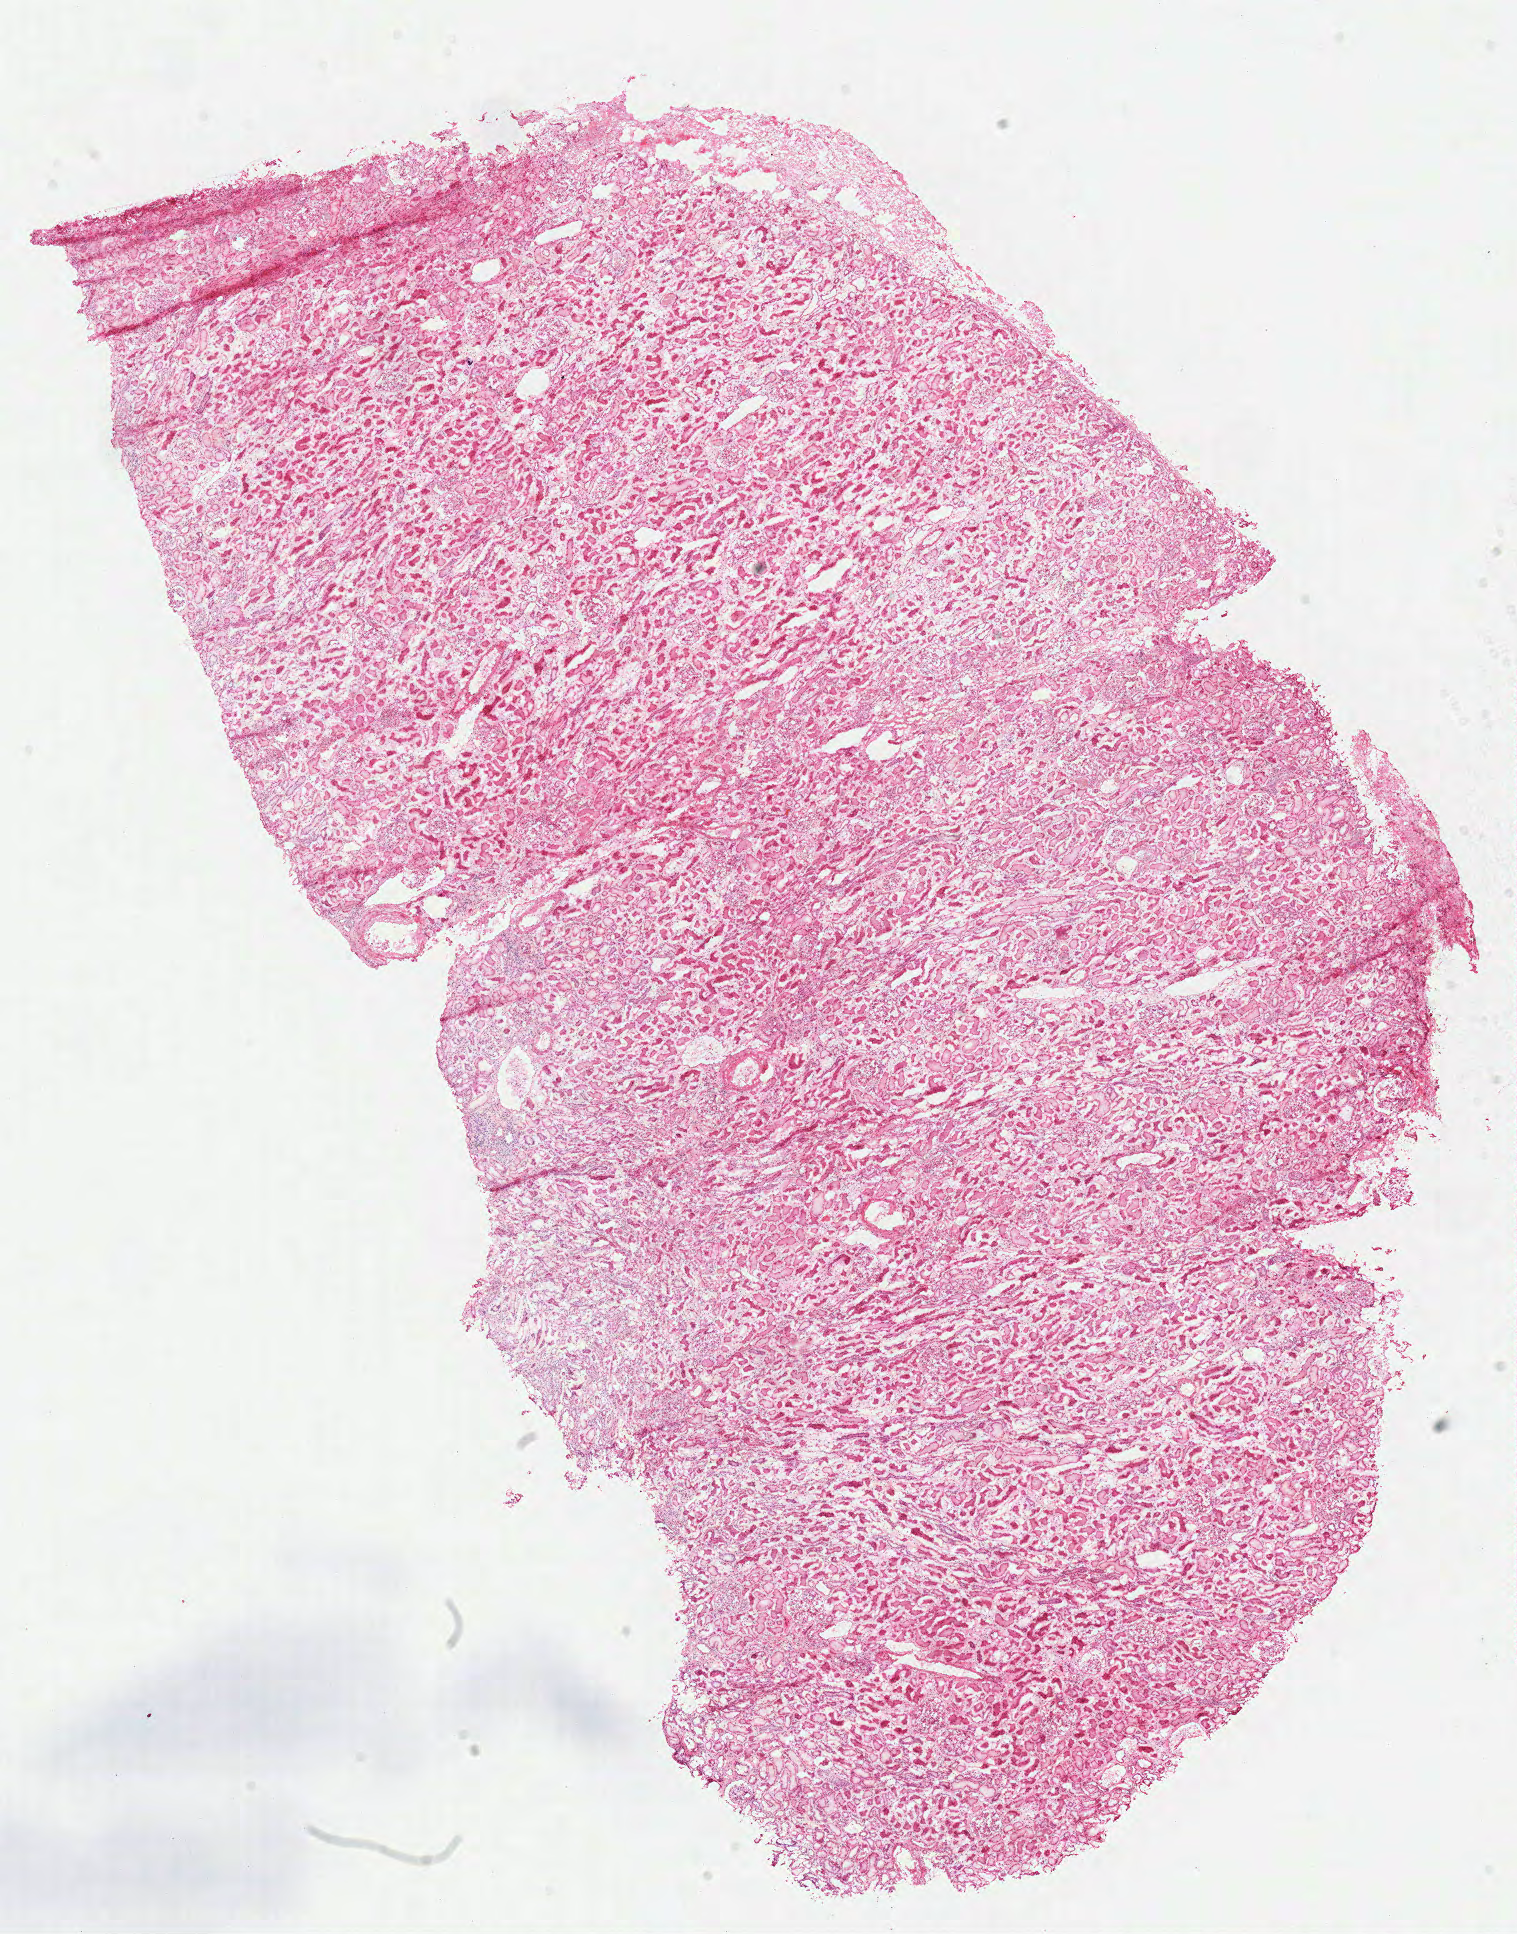
Digitized H&E tissue section (whole slide) — shown as a low-resolution overview of the whole scanned area (about 12.0 x 15.2 mm), frozen section, solid tissue normal (non-tumour tissue) sample from the kidney. Male, age 42 years at initial diagnosis.
This section: solid tissue normal sample (biorepository sample class). Patient diagnosis: Papillary adenocarcinoma, NOS.